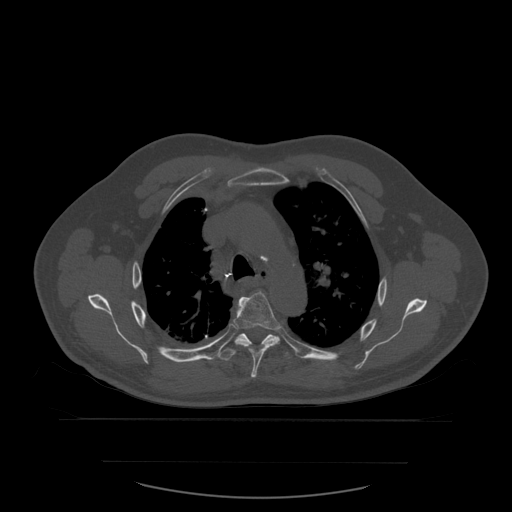
CT including the spine, one axial slice. Slice 418 of 590 in the series (ordered by position). Bone window (W 1800 / L 400 HU). 1.25 mm slice thickness. 512 × 512 image matrix, field of view 479 × 479 mm. Patient age 71 years. Case-level facts recorded for this patient, not image findings: primary cancer: lung; vertebrae with lytic lesions (as recorded): T1, T2, L5, S1.
Outlined on this slice (semi-automatically segmented with operator editing):
- T5 vertebra: bounding box <233,292,280,379> (left, top, right, bottom; pixels)
- T6 vertebra: <220,333,288,361>